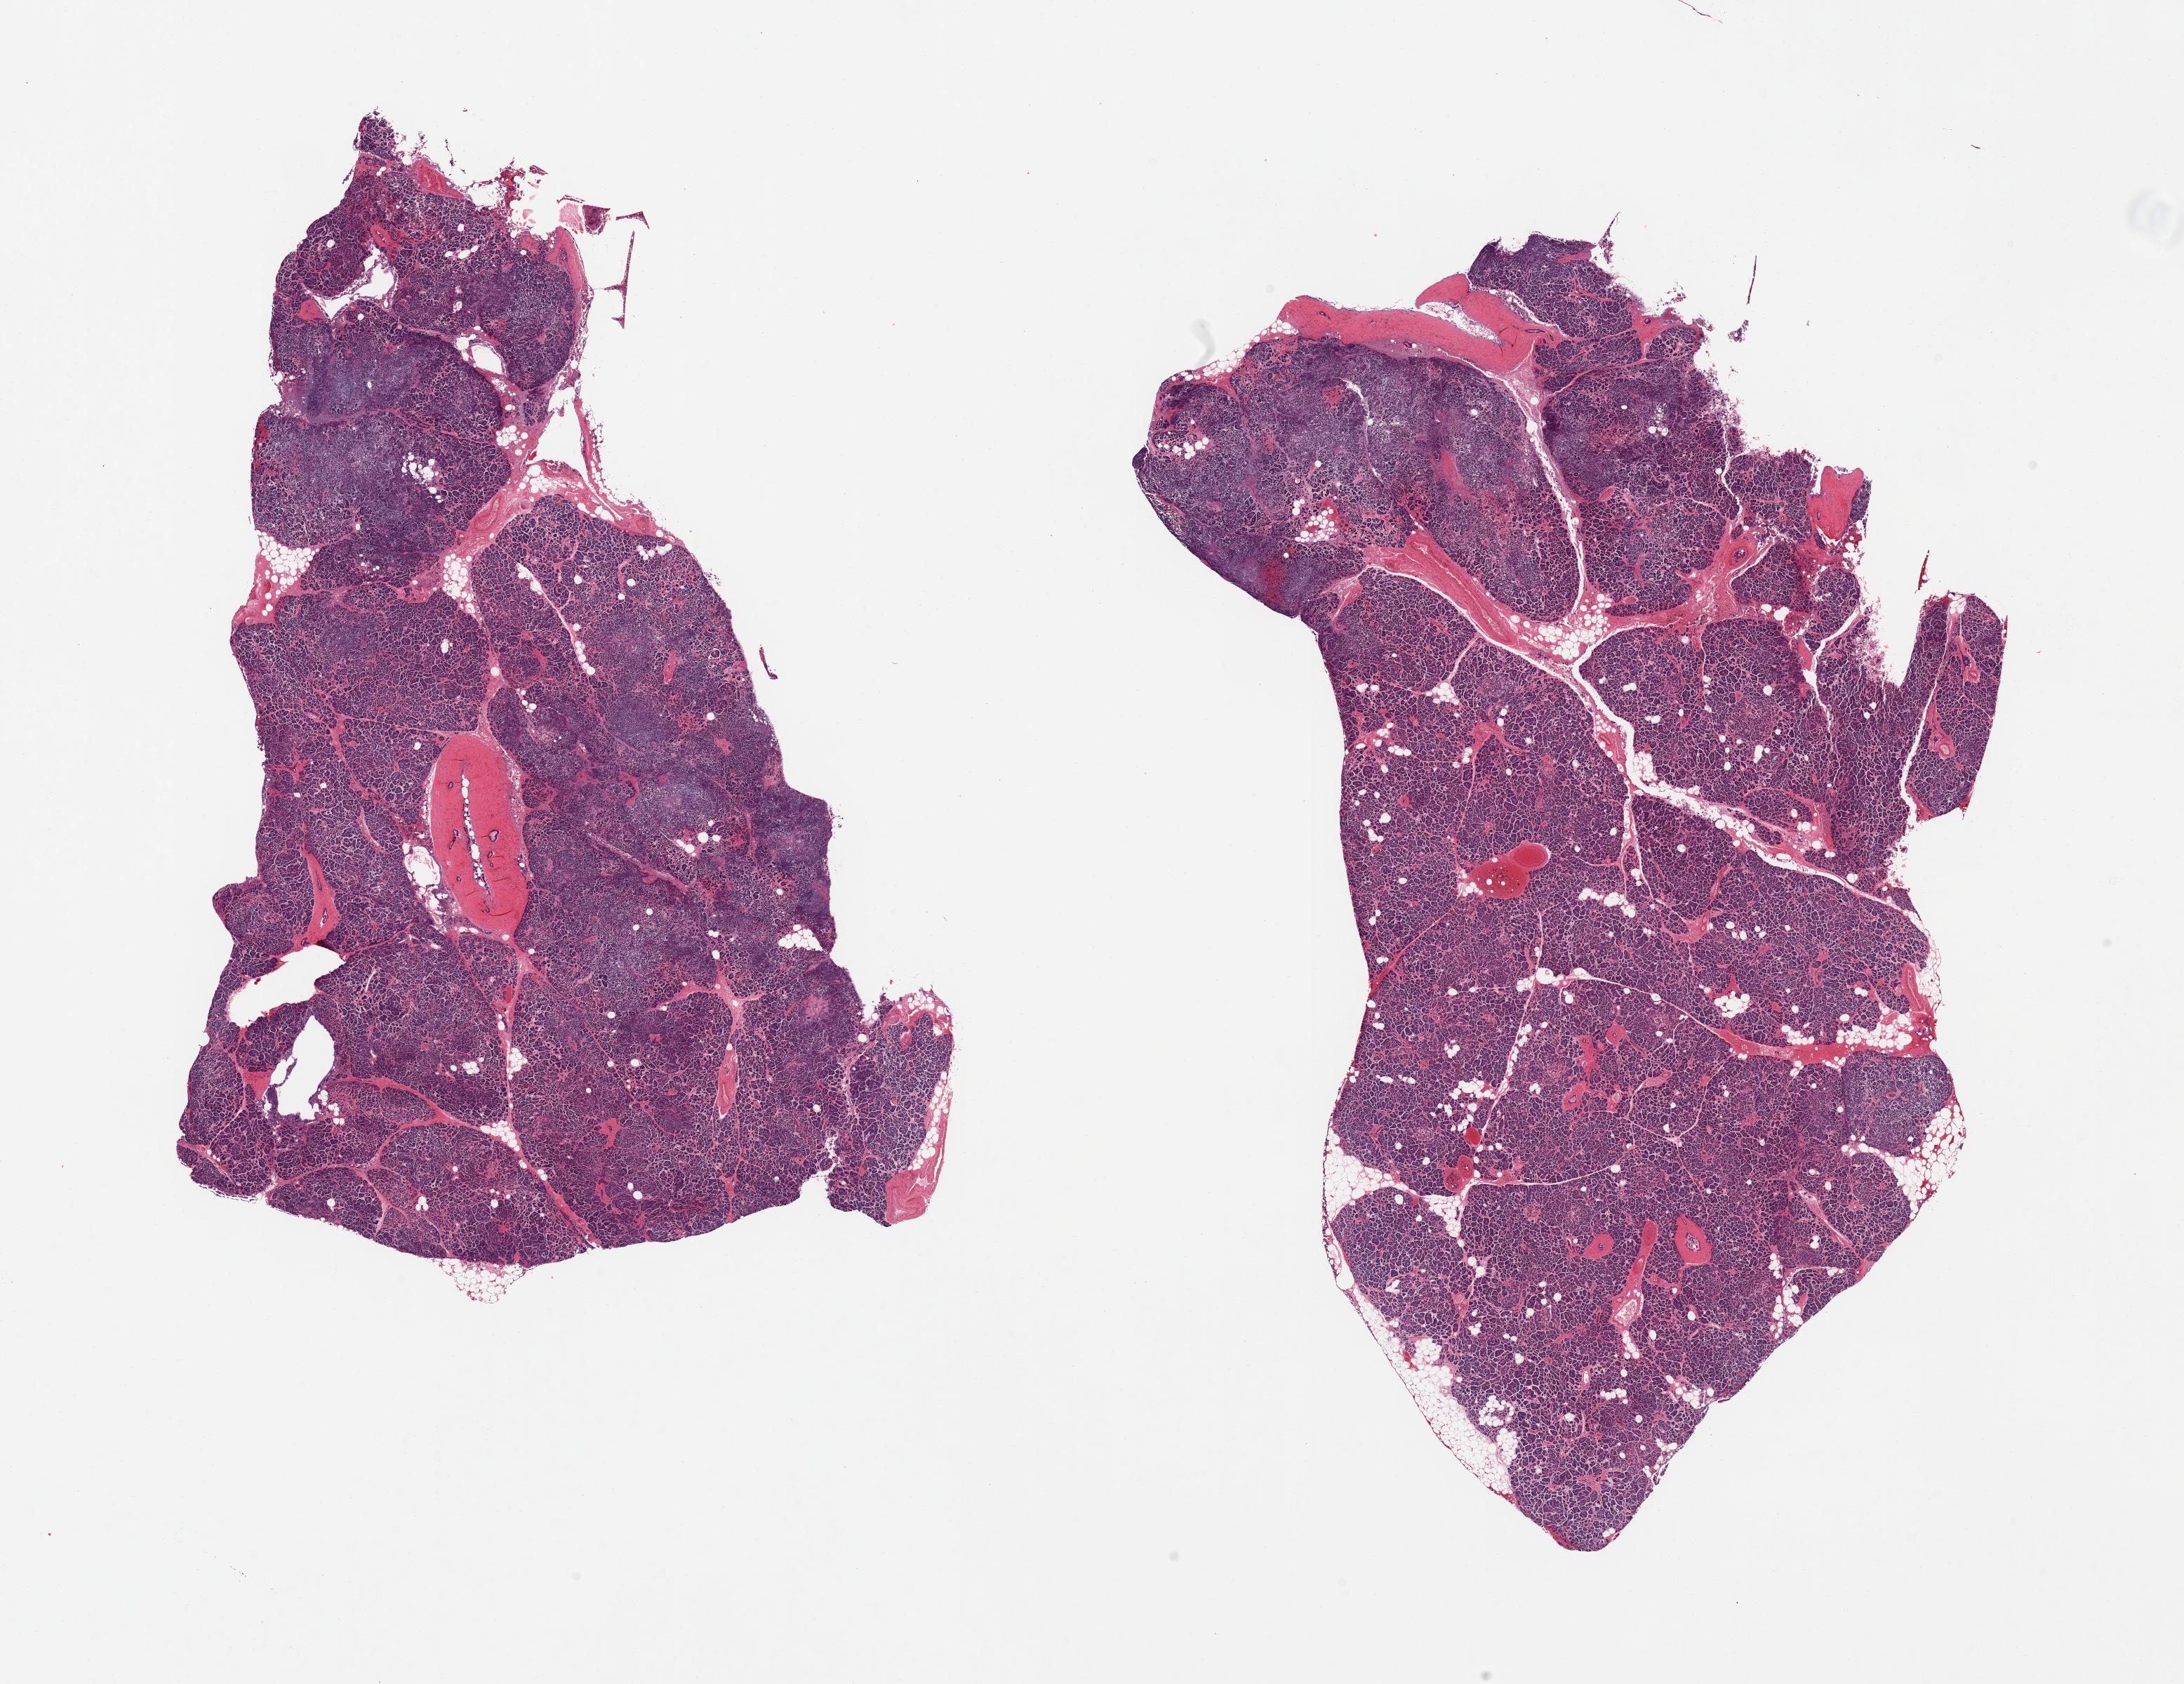
Whole-slide image, haematoxylin and eosin stain, shown as a low-resolution overview of the whole scanned area (about 24.6 x 19.0 mm); PAXgene-fixed, paraffin-embedded tissue; section of pancreas (target tissue); donor tissue sample. Donor sex: male.
Review note (as recorded): 2 pieces; well trimmed; 5% internal fat.